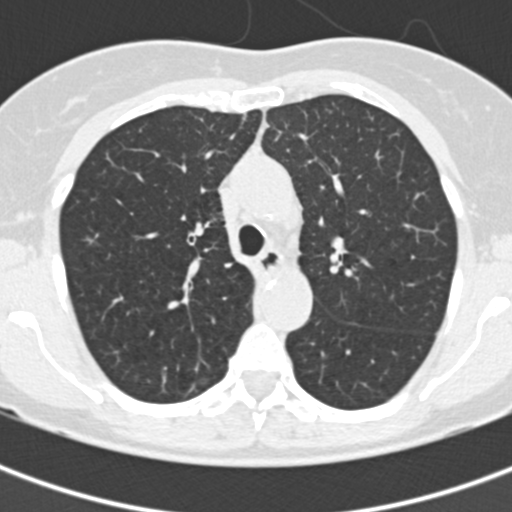
Axial slice from a low-dose chest CT screening exam, baseline screening round, lung window (W 1500 / L -600 HU), standard (soft-tissue) reconstruction kernel (B30f), slice 60 of 177 in the series. Female, age 60 years at enrolment. Current smoker at enrolment.
Lesion marked by an expert reader, bounding box (x1, y1, x2, y2) in pixels: (66, 220, 111, 271). No non-calcified nodule or mass ≥4 mm was recorded by the screening reader at this exam. Official screen result: negative screen, no significant abnormalities. Participant outcome: lung cancer diagnosed 861 days after this screen — bronchiolo-alveolar adenocarcinoma, NOS, right upper lobe, well differentiated (G1), stage IA (AJCC 6th edition), 11 mm at pathology.